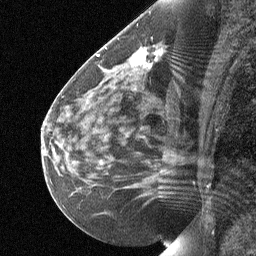
Breast MRI (dynamic contrast-enhanced), one sagittal slice; position 33 of 64 along the scan axis; dynamic contrast-enhanced study with each time point stored as its own series, time point 2 of 3 at this slice position (early post-contrast, ordered by acquisition time); 1.5 T; TE 4.8 ms, TR 27 ms; 2 mm slice thickness; 256 × 256 image matrix, field of view 180 × 180 mm. Patient: female, 51 years. Case-level facts recorded for this patient, not image findings: setting: breast cancer imaged before/during neoadjuvant chemotherapy; receptor status: HR-positive, HER2-negative.
Annotated regions visible in this slice (semi-automatic segmentation, software-assisted and operator-edited):
- analysis volume of interest (the breast-tissue region the enhancement analysis was run in; not a lesion): bounding box <81,35,179,103> (left, top, right, bottom; pixels)
- tumour enhancement mask (voxels above the 90 % enhancement threshold inside the analysis volume of interest): <136,51,157,58>